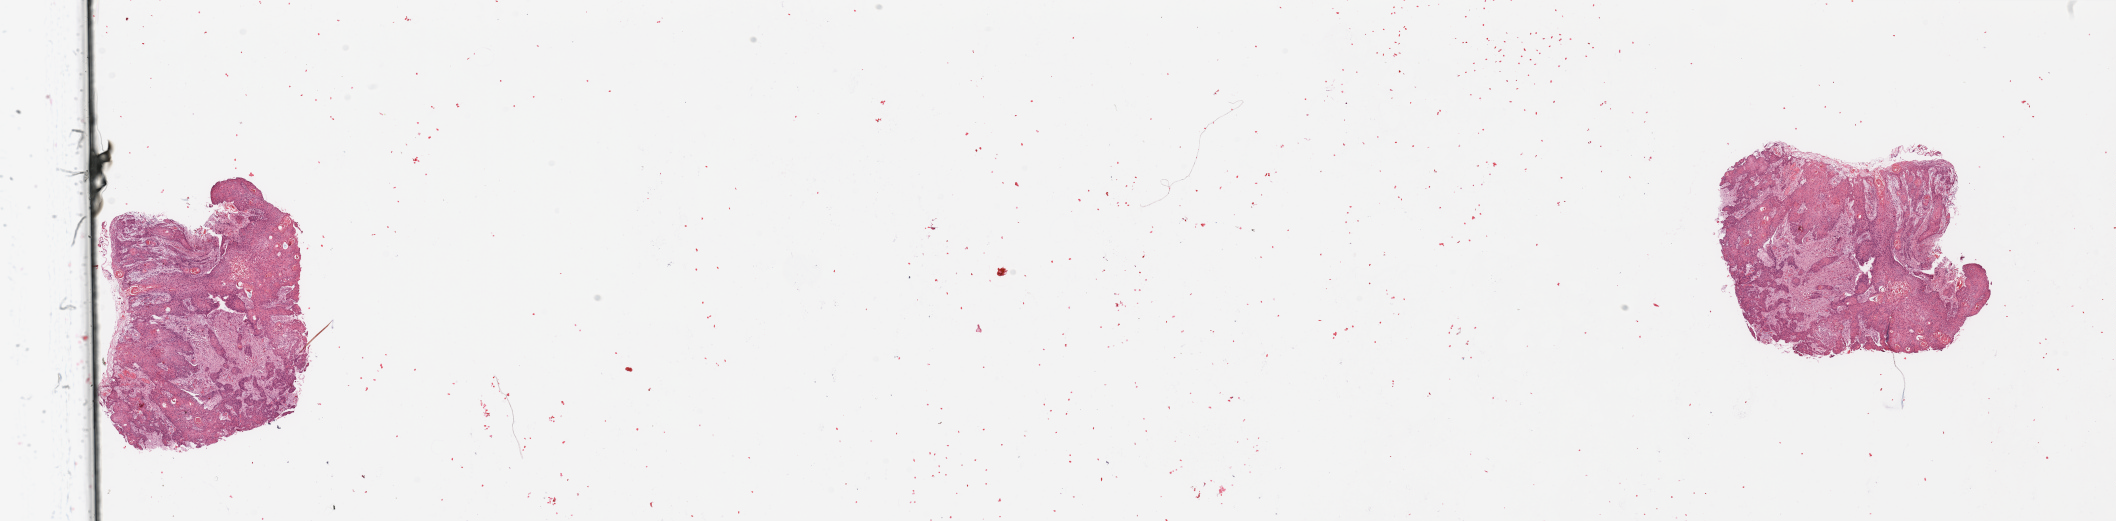
H&E whole-slide image — a low-resolution overview of the entire scanned area, about 33.5 x 8.2 mm (from a 20x scan), head and neck, tissue type not recorded. 59-year-old male patient.
Patient diagnosis: Squamous cell carcinoma, NOS (floor of mouth, NOS).